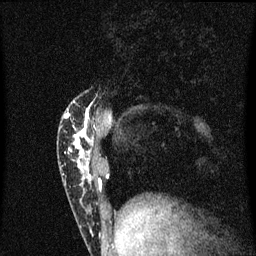
Breast MRI (dynamic contrast-enhanced), one sagittal slice; slice 16 of 60 in the series (ordered by position); dynamic contrast-enhanced series, image 2 of 3 at this slice position (ordered by acquisition); 1.5 T; TE 4.2 ms, TR 8.4 ms; 2 mm slice thickness; 256 × 256 image matrix, field of view 200 × 200 mm. Patient: female, 40 years.
Structures marked on this image (semi-automatically segmented with operator editing):
- analysis volume of interest (the breast-tissue region the enhancement analysis was run in; not a lesion): bounding box (x1, y1, x2, y2) in pixels: (59, 98, 103, 201)
- tumour enhancement mask (voxels above the 70 % enhancement threshold inside the analysis volume of interest): (65, 102, 94, 181)